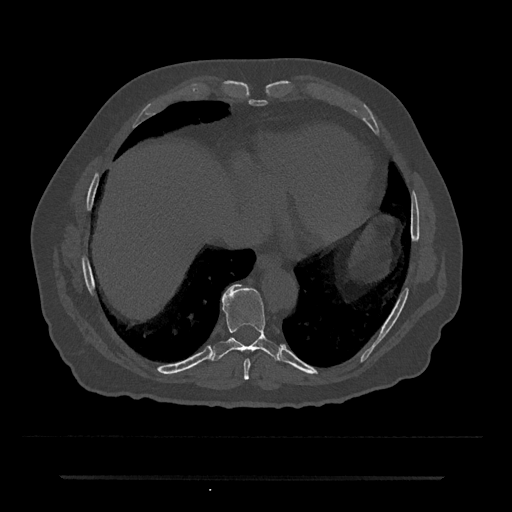
CT including the spine, one axial slice; slice 285 of 797 in the series (ordered by position); 120 kVp; bone window (W 1800 / L 400 HU); 0.5 mm slice thickness; 512 × 512 image matrix, field of view 437 × 437 mm. Patient: male, 69 years. Case-level facts recorded for this patient, not image findings: primary cancer: prostate.
Annotated regions visible in this slice (semi-automatically segmented with operator editing):
- T8 vertebra: bounding box <244,359,251,380> (left, top, right, bottom; pixels)
- T9 vertebra: <212,284,282,362>